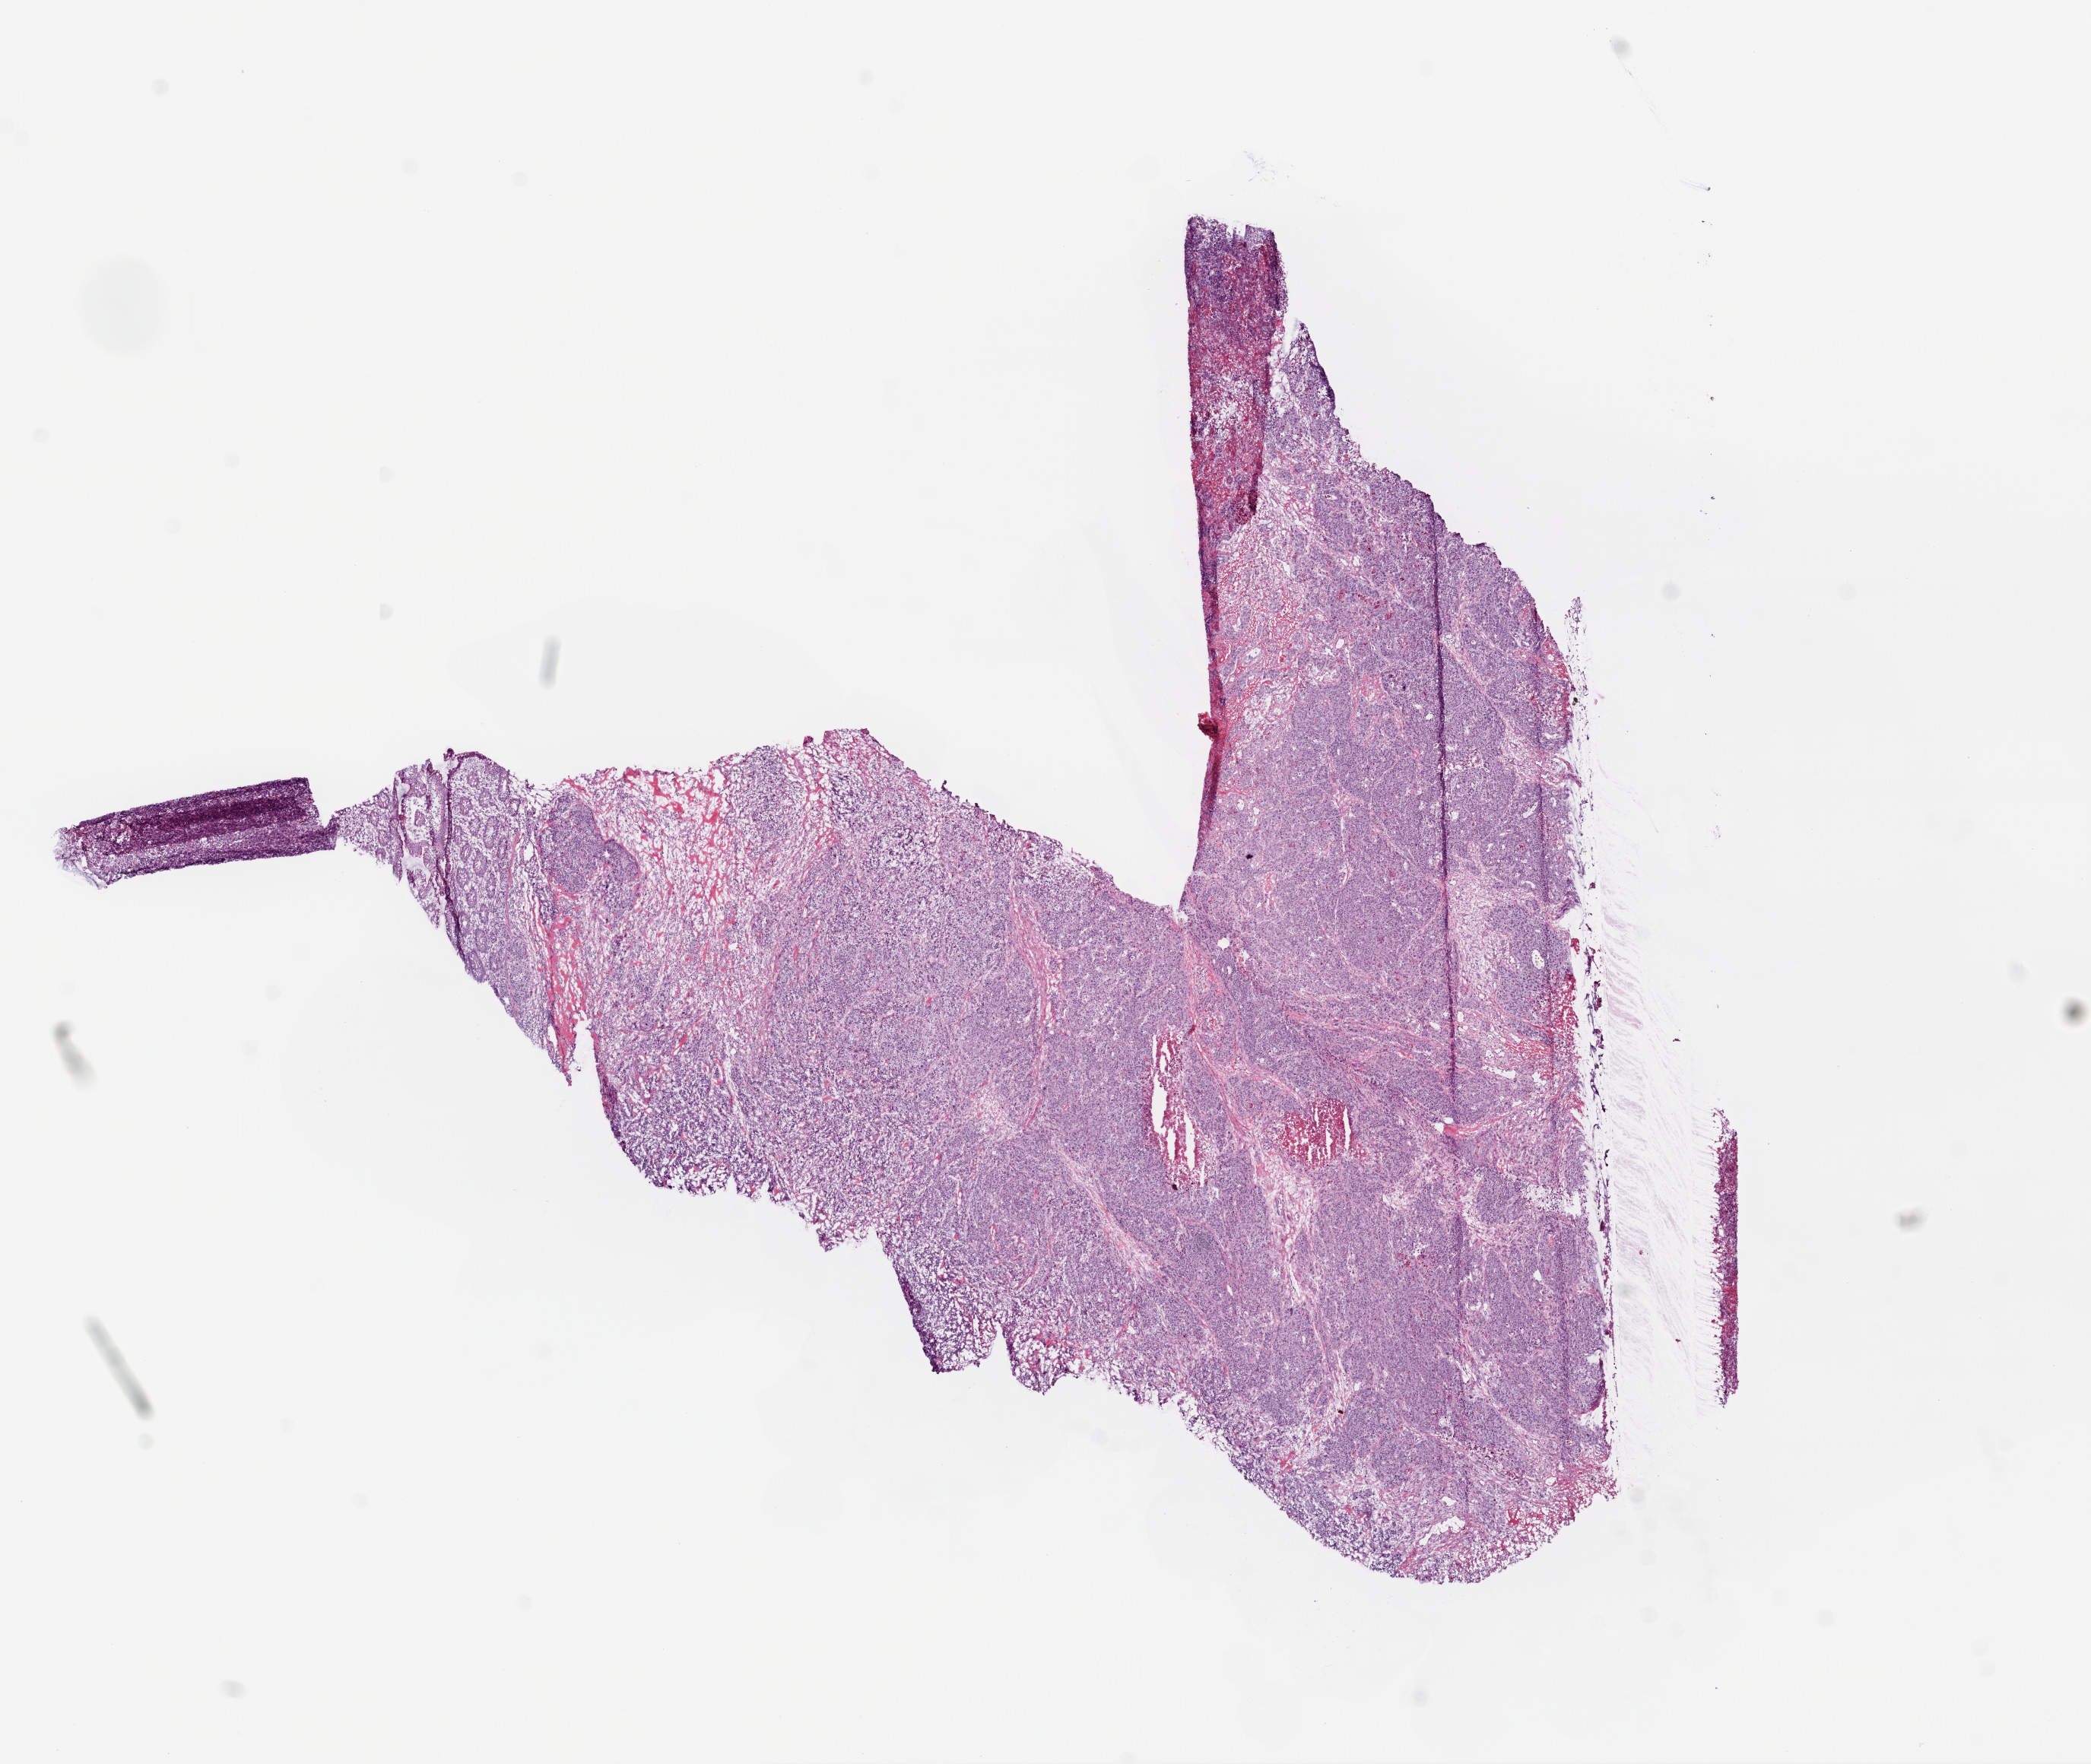
Digitized H&E-stained tissue section (whole slide), a low-resolution overview of the entire scanned area, about 11.0 x 9.3 mm. Frozen section from the top of the tissue portion. Colon, primary tumour sample. Male, age 66 years at initial diagnosis. Slide review estimates, as recorded: tumour cells 85%, tumour nuclei 85%, normal cells 5%, stromal cells 5%, necrosis 5%.
- diagnosis: Adenocarcinoma, NOS
- AJCC pathologic stage: IV
- lymph nodes positive (case pathology): 24 of 29 examined